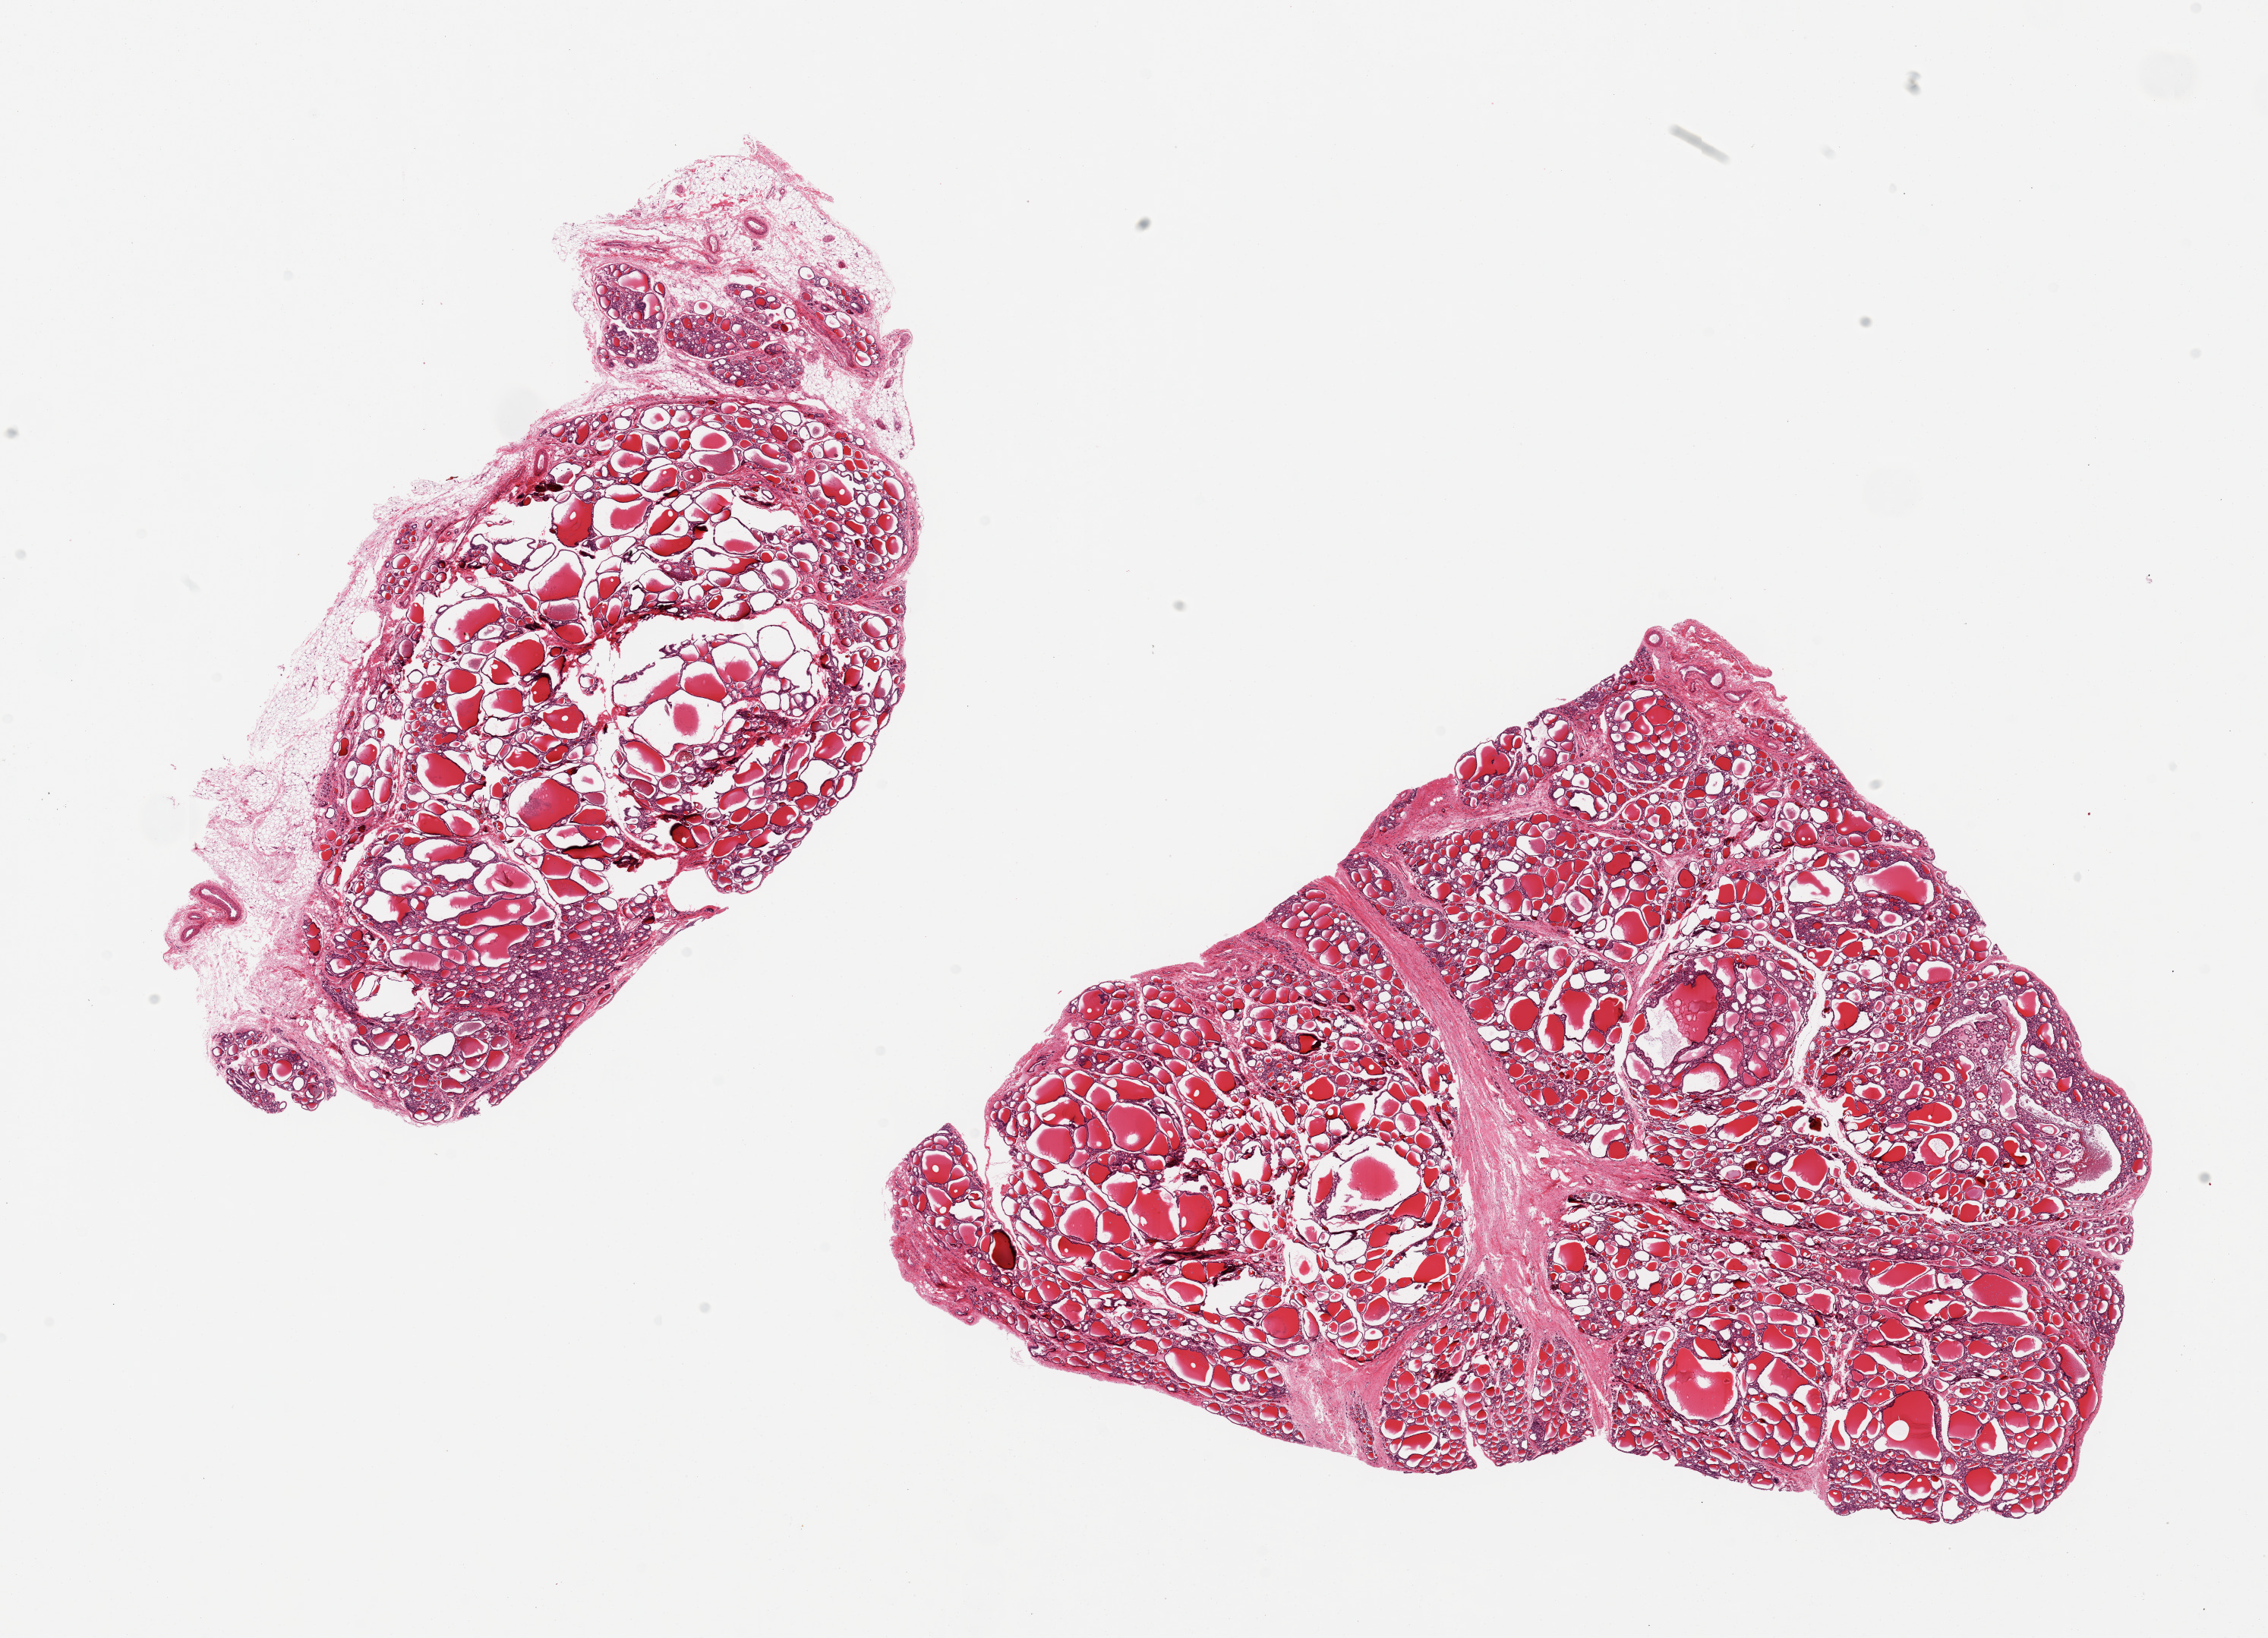
Whole-slide image, haematoxylin and eosin stain, brightfield — low-resolution overview of the scanned area, about 23.6 x 17.1 mm; PAXgene-fixed, paraffin-embedded tissue; target tissue: thyroid; donor tissue sample. Female donor.
Reviewer comment on this tissue sample: 2 pieces; 1 piece has 20% external fat.